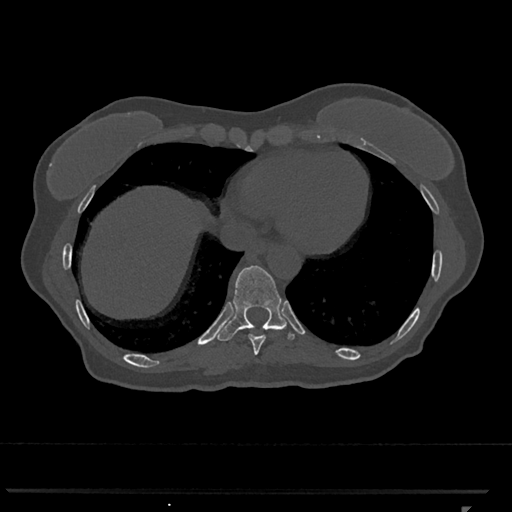
CT including the spine, one axial slice. Position 587 of 793 along the scan axis. Reconstruction kernel Br40s/3. 120 kVp. Bone window (W 1800 / L 400 HU). 0.5 mm slice thickness. 512 × 512 image matrix, field of view 380 × 380 mm. Patient: female, 62 years. From the clinical record (not read from this slice): primary cancer: renal.
Annotated regions visible in this slice (semi-automatically segmented with operator editing):
- T10 vertebra: bounding box [x1, y1, x2, y2] px = [217, 266, 295, 341]
- T9 vertebra: [249, 330, 267, 355]